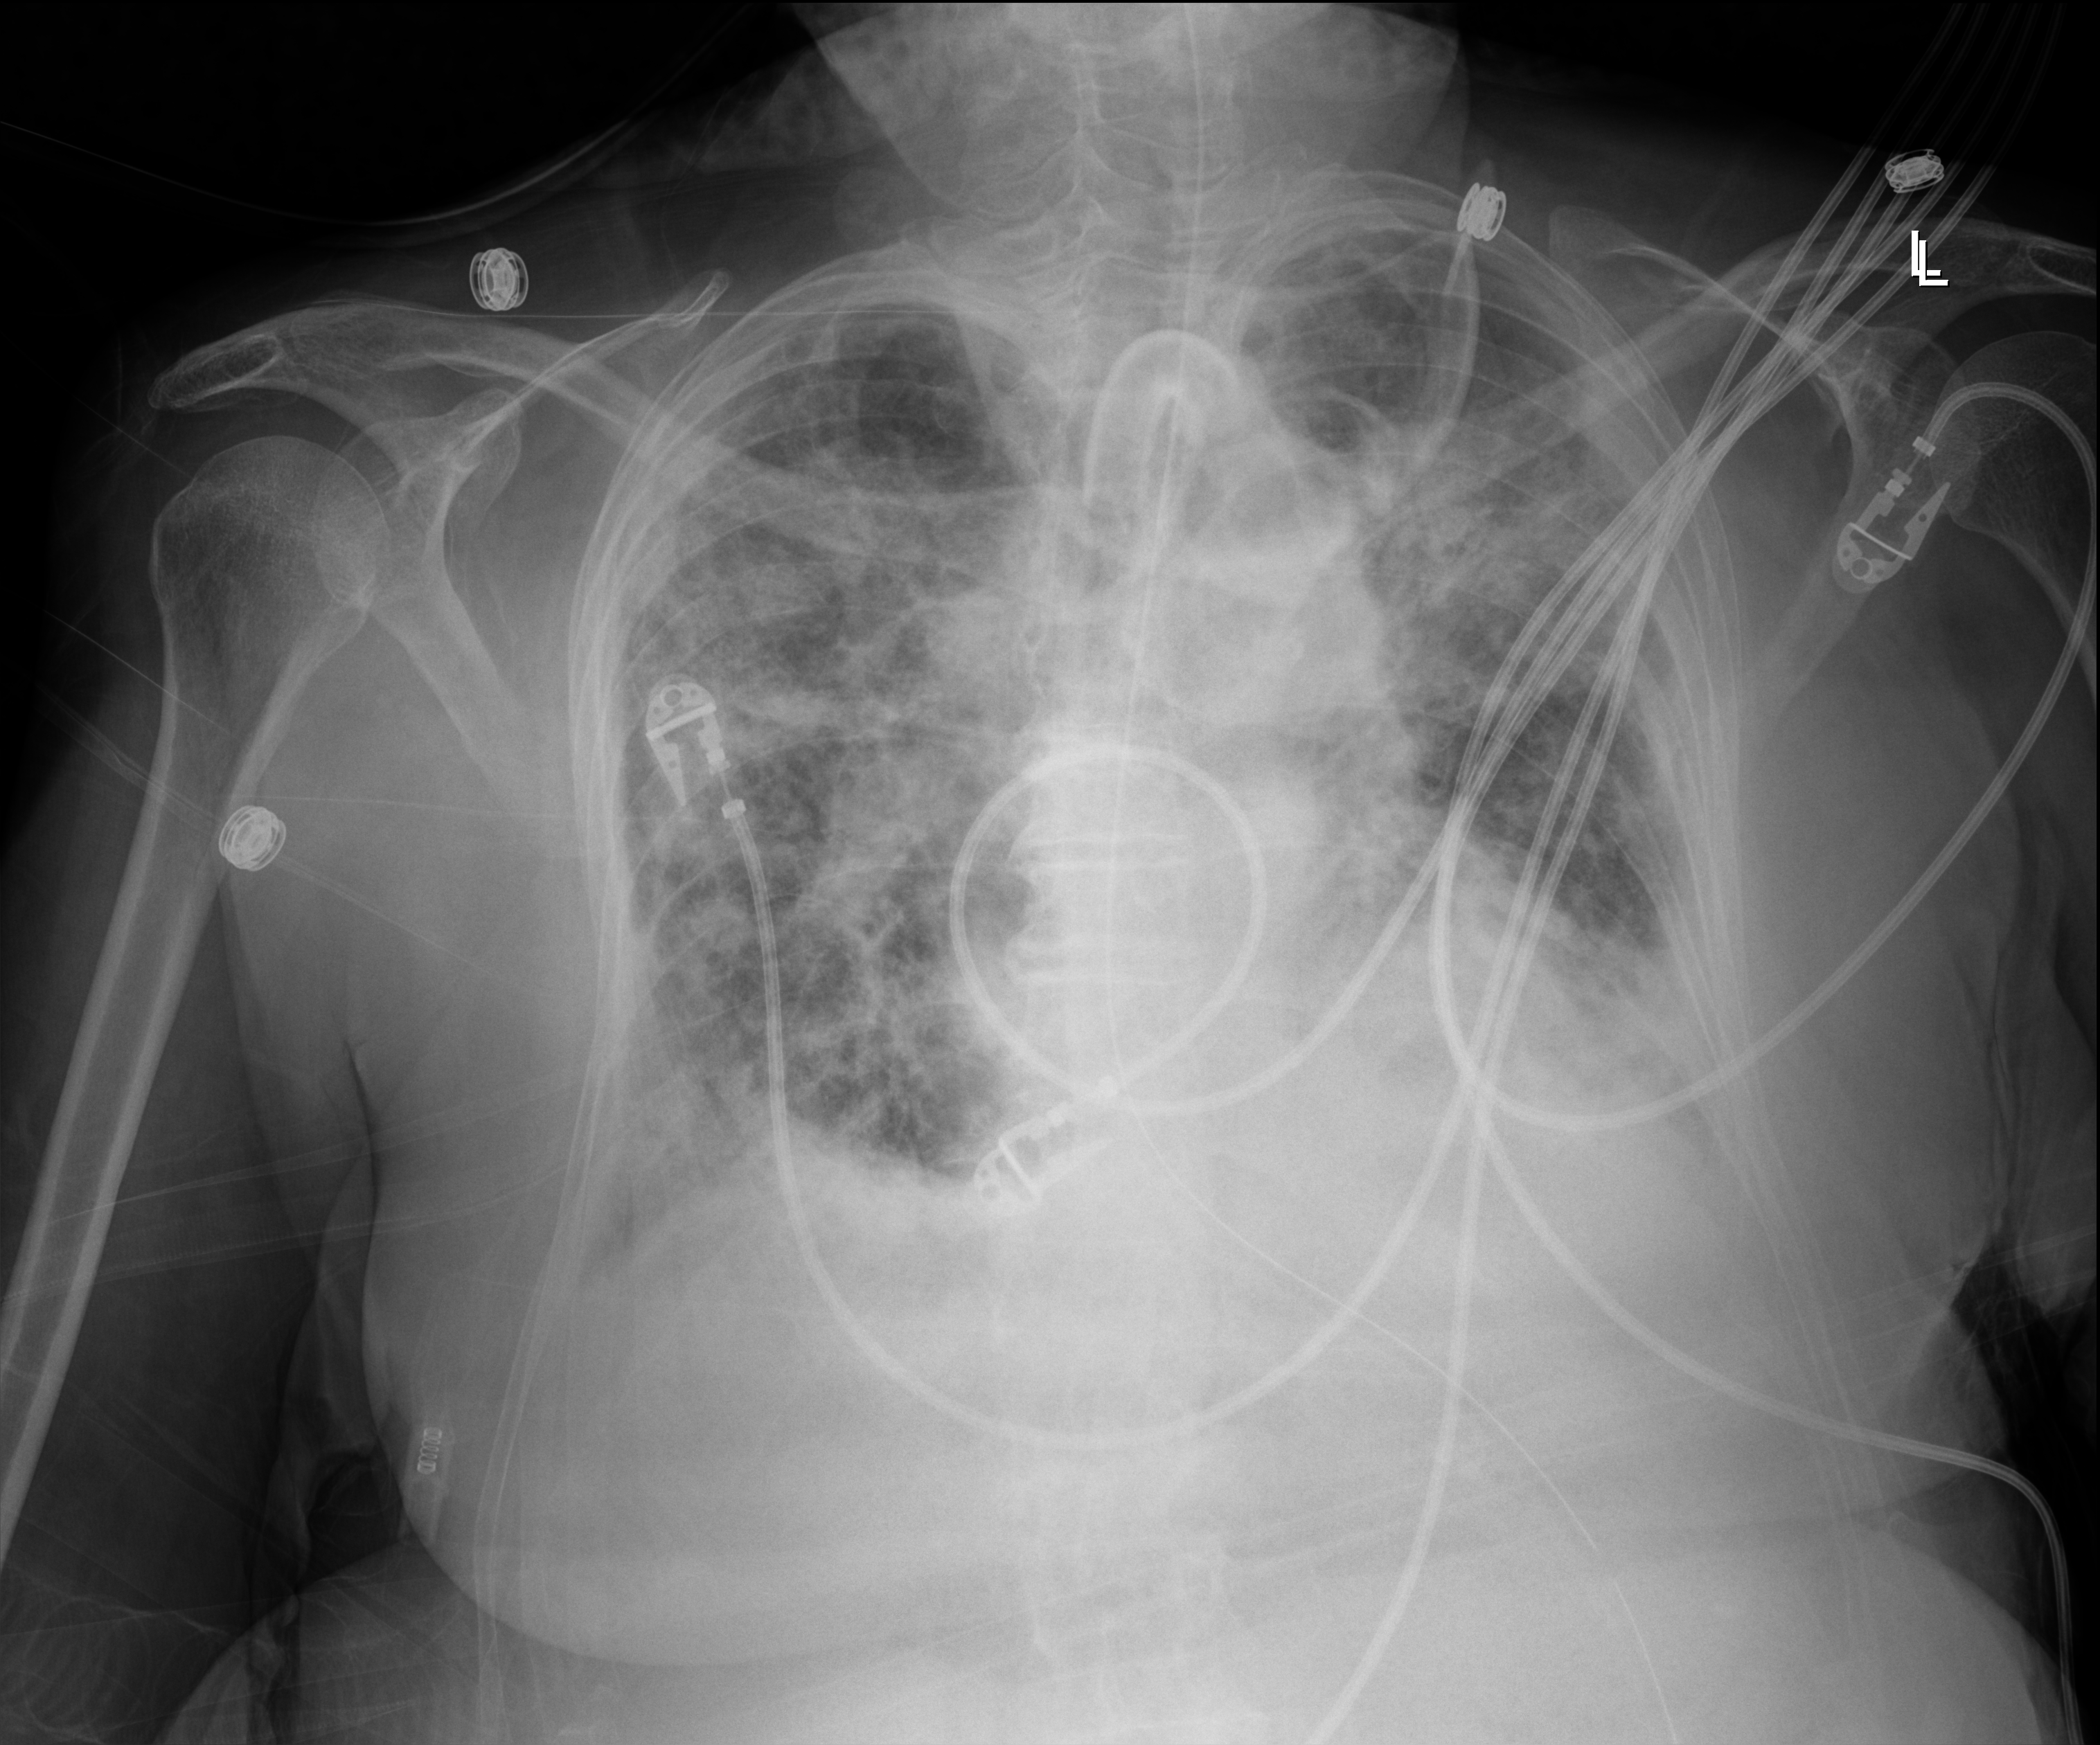
Chest X-ray (portable). Female patient hospitalised with COVID-19, age 75–90 years.
Hospital-stay facts (about this admission, not read from this image; timing relative to this image not recorded): chronic kidney disease (admission record): no; hypertension (admission record): yes.